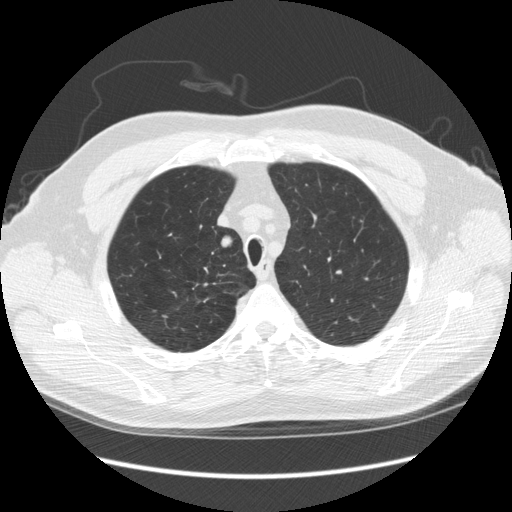
Chest CT (low-dose screening protocol), one axial image, third screening round (two years after baseline), lung window (W 1500 / L -600 HU), 2.5 mm slice thickness. Male participant, aged 64 years at enrolment.
- Expert-annotated lung lesion, bounding box (x1, y1, x2, y2) in pixels: (197, 230, 240, 263).
- The screening reader recorded 4 non-calcified nodules or masses ≥4 mm on this exam (right upper lobe, right upper lobe, right upper lobe, right upper lobe); which of them this box marks is not recorded.
- Official screen result: positive, other.
- Participant outcome: lung cancer diagnosed 15 days after this screen — adenocarcinoma, NOS, right upper lobe, moderately differentiated (G2), stage IA (AJCC 6th edition), 14 mm at pathology.